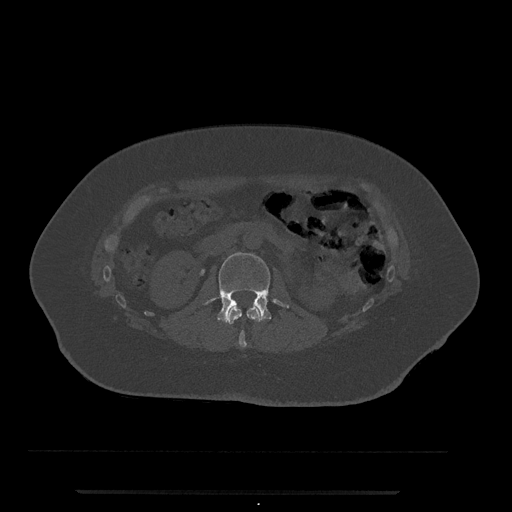
CT including the spine, one axial slice. Slice 57 of 797 in the series (ordered by position). Reconstruction kernel Br40s/3. 120 kVp. Bone window (W 1800 / L 400 HU). 0.5 mm slice thickness. 512 × 512 image matrix, field of view 440 × 440 mm. Female patient, age 51 years. Case-level facts recorded for this patient, not image findings: primary cancer: neuro; vertebrae with lytic lesions (as recorded): T8.
Outlined on this slice (semi-automatically segmented with operator editing):
- L1 vertebra: bounding box <226,307,261,348> (left, top, right, bottom; pixels)
- L2 vertebra: <203,252,289,323>